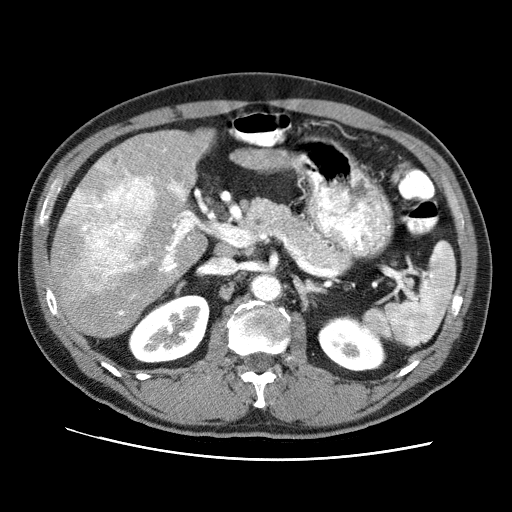
Contrast-enhanced abdominal CT (liver protocol), one axial slice. Position 41 of 71 along the scan axis. Reconstruction kernel STANDARD. 120 kVp. Soft-tissue window (W 400 / L 40 HU). 512 × 512 image matrix, field of view 360 × 360 mm. Case-level facts recorded for this patient, not image findings: diagnosis: hepatocellular carcinoma (patient treated with transarterial chemoembolisation; whether this scan precedes or follows treatment is not stated here); TNM stage (as recorded): Stage-II; Child-Pugh class: A; tumour nodularity: multinodular; tumour size: 4.6 cm.
Annotated regions visible in this slice (semi-automatic segmentation, software-assisted and operator-edited):
- liver parenchyma outside the tumour (the mass and vessels are separate outlines, so this box may not span the whole liver): box from (x=50, y=130) to (x=270, y=338) px
- mass: (x=60, y=171)–(x=157, y=297)
- liver vessels: (x=96, y=149)–(x=182, y=315)